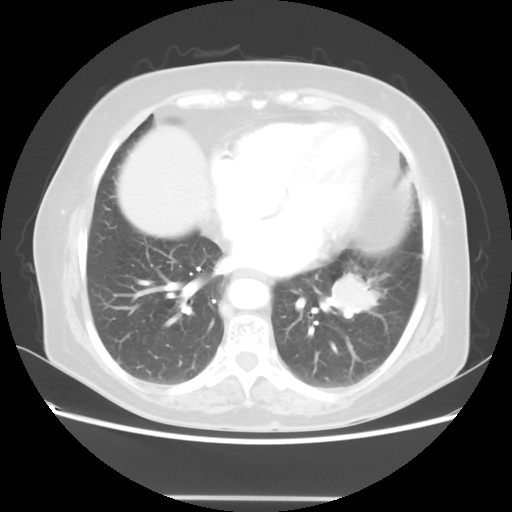
Chest CT, one axial slice; position 21 of 56 along the scan axis; 100 kVp; lung window (W 1500 / L -600 HU); 512 × 512 image matrix, field of view 360 × 360 mm. Female patient, age 73 years. From the clinical record (not read from this slice): clinical TNM (as recorded): T1c N0 M0.
Annotated regions visible in this slice (rectangle marked by the reading radiologist):
- lung tumour (recorded histology: adenocarcinoma): box from (x=332, y=268) to (x=378, y=323) px